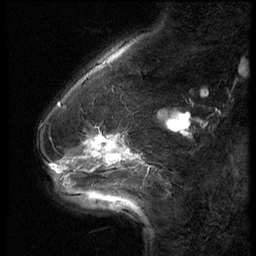
Breast MRI (dynamic contrast-enhanced), one sagittal slice. Position 17 of 62 along the scan axis. 3 images stored at this slice position (order not interpretable as contrast timing). 1.5 T. TE 4.2 ms, TR 9 ms. 2.5 mm slice thickness. 256 × 256 image matrix, field of view 180 × 180 mm. Patient: female, 54 years. Case-level facts recorded for this patient, not image findings: setting: breast cancer imaged before/during neoadjuvant chemotherapy; receptor status: HR-positive, HER2-negative.
Structures marked on this image (semi-automatically segmented with operator editing):
- analysis volume of interest (the breast-tissue region the enhancement analysis was run in; not a lesion): bounding box (x1, y1, x2, y2) in pixels: (42, 126, 146, 183)
- tumour enhancement mask (voxels above the 140 % enhancement threshold inside the analysis volume of interest): (94, 136, 117, 156)